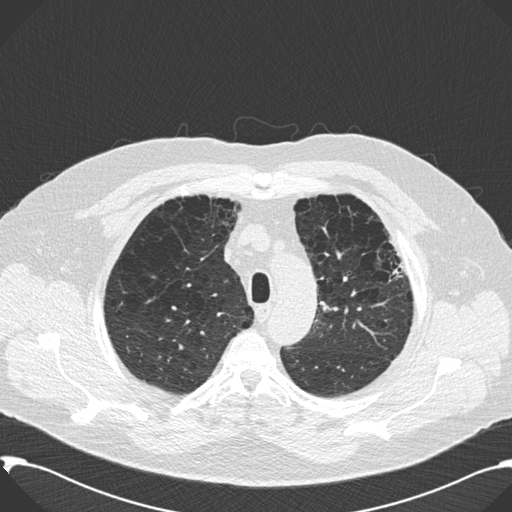
Low-dose screening chest CT, axial slice; second annual screen; lung window (W 1500 / L -600 HU); slice 37 of 199 in the series; 512 × 512 image matrix, field of view 380 × 380 mm. Male participant, aged 59 years at enrolment.
Expert reader's lesion annotation, bounding box [x1, y1, x2, y2] px = [365, 232, 414, 302]. Screening reader's record for this exam: no non-calcified nodule ≥4 mm recorded. Official screen result: negative screen, significant abnormalities not suspicious for lung cancer. Later outcome: lung cancer diagnosed 518 days after this screen (after the third annual screen) — bronchiolo-alveolar carcinoma, mixed mucinous and non-mucinous, left upper lobe, stage IA (AJCC 6th edition), 20 mm at pathology.